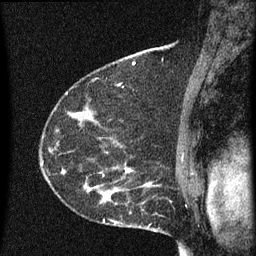
Breast MRI (dynamic contrast-enhanced), one sagittal slice; position 42 of 60 along the scan axis; dynamic contrast-enhanced series, image 2 of 3 at this slice position (ordered by acquisition); 1.5 T; TE 4.2 ms, TR 8 ms; 256 × 256 image matrix, field of view 180 × 180 mm. Female patient, age 55 years.
Structures marked on this image (semi-automatic segmentation, software-assisted and operator-edited):
- analysis volume of interest (the breast-tissue region the enhancement analysis was run in; not a lesion): bounding box [x1, y1, x2, y2] px = [51, 156, 145, 217]
- tumour enhancement mask (voxels above the 70 % enhancement threshold inside the analysis volume of interest): [84, 168, 145, 203]